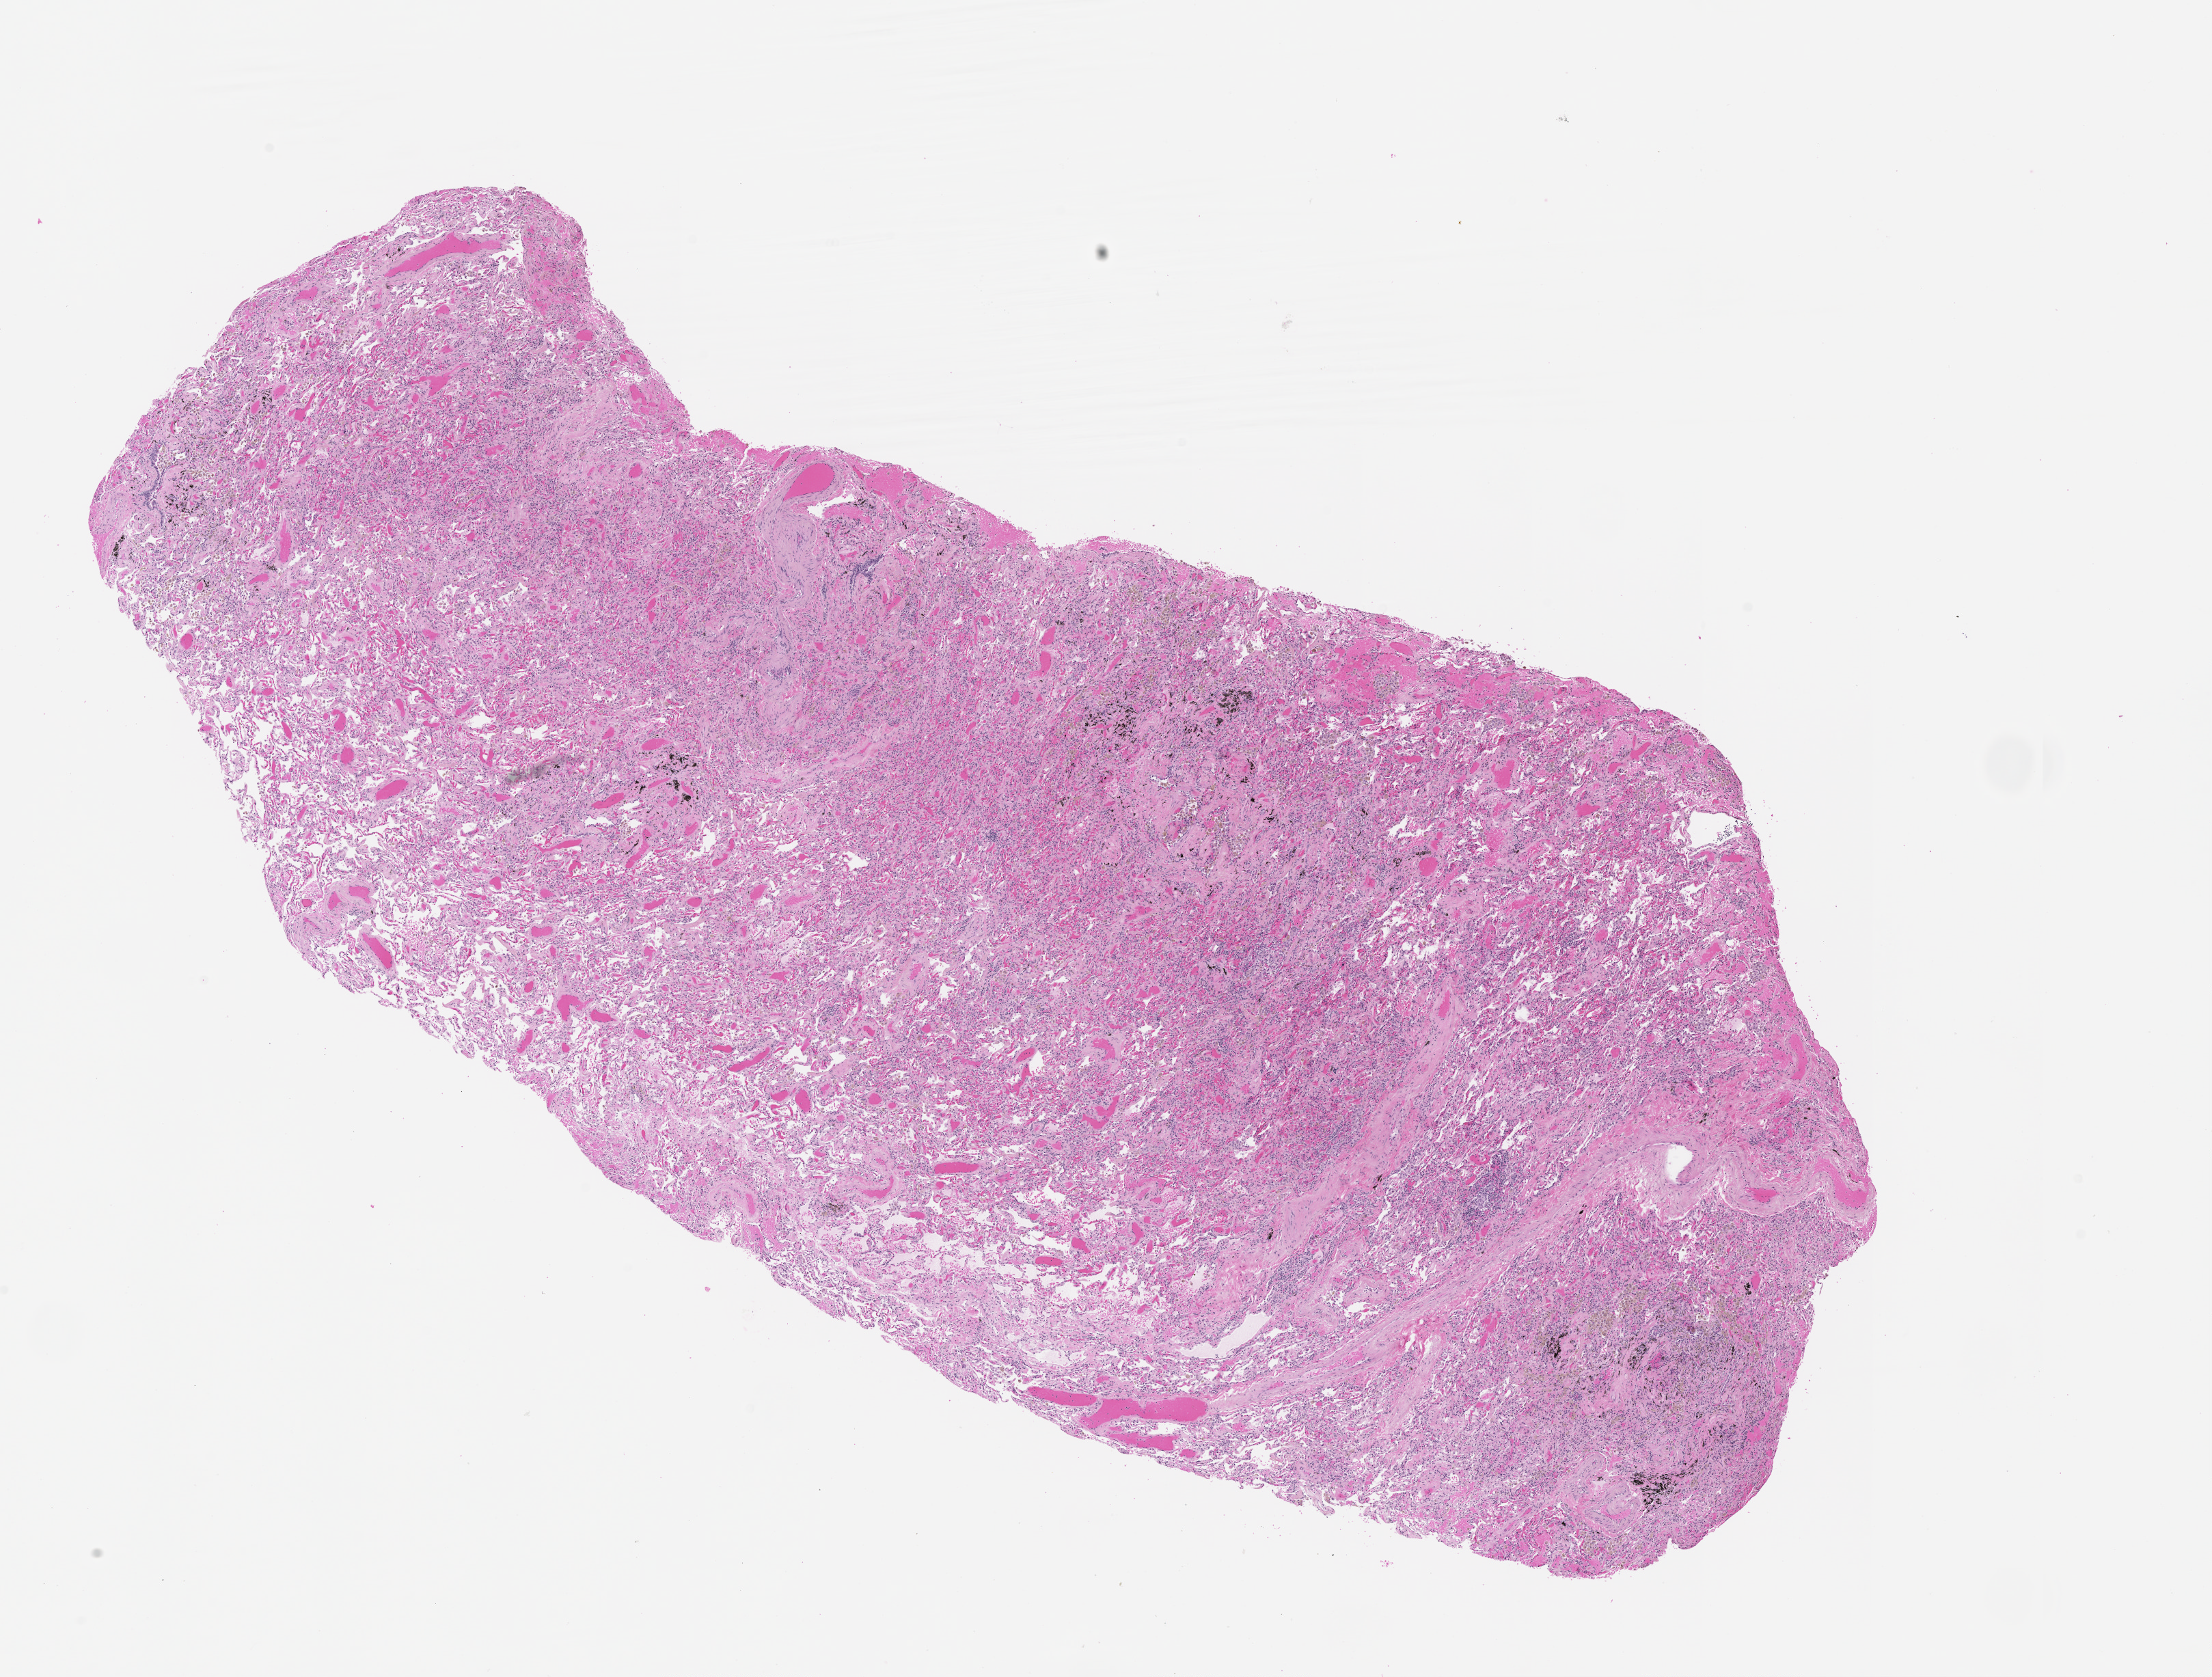
Whole-slide histology image, H&E-stained — low-resolution overview of the scanned area, about 13.0 x 9.9 mm (acquisition: 20x scan); lung, tissue type not recorded.
* patient diagnosis (cohort enrolment): squamous cell carcinoma (lung)